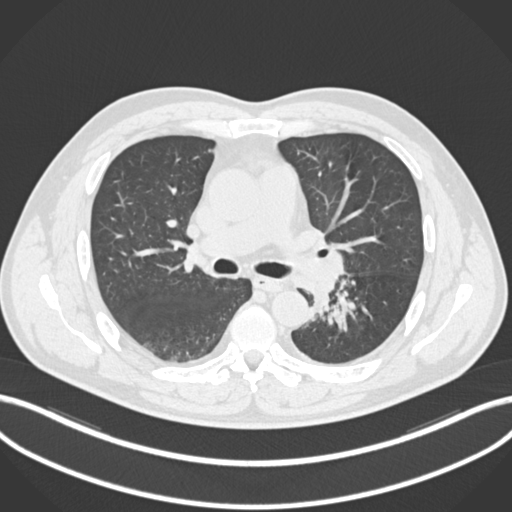
Chest CT, one axial slice. Position 137 of 223 along the scan axis. 120 kVp. Lung window (W 1500 / L -600 HU). 1 mm slice thickness. 512 × 512 image matrix, field of view 400 × 400 mm. Male patient, age 50 years. Case-level facts recorded for this patient, not image findings: clinical TNM (as recorded): T2a N3 M0.
Annotated regions visible in this slice (rectangle marked by the reading radiologist):
- lung tumour (recorded histology: squamous cell carcinoma): box from (x=310, y=277) to (x=358, y=333) px